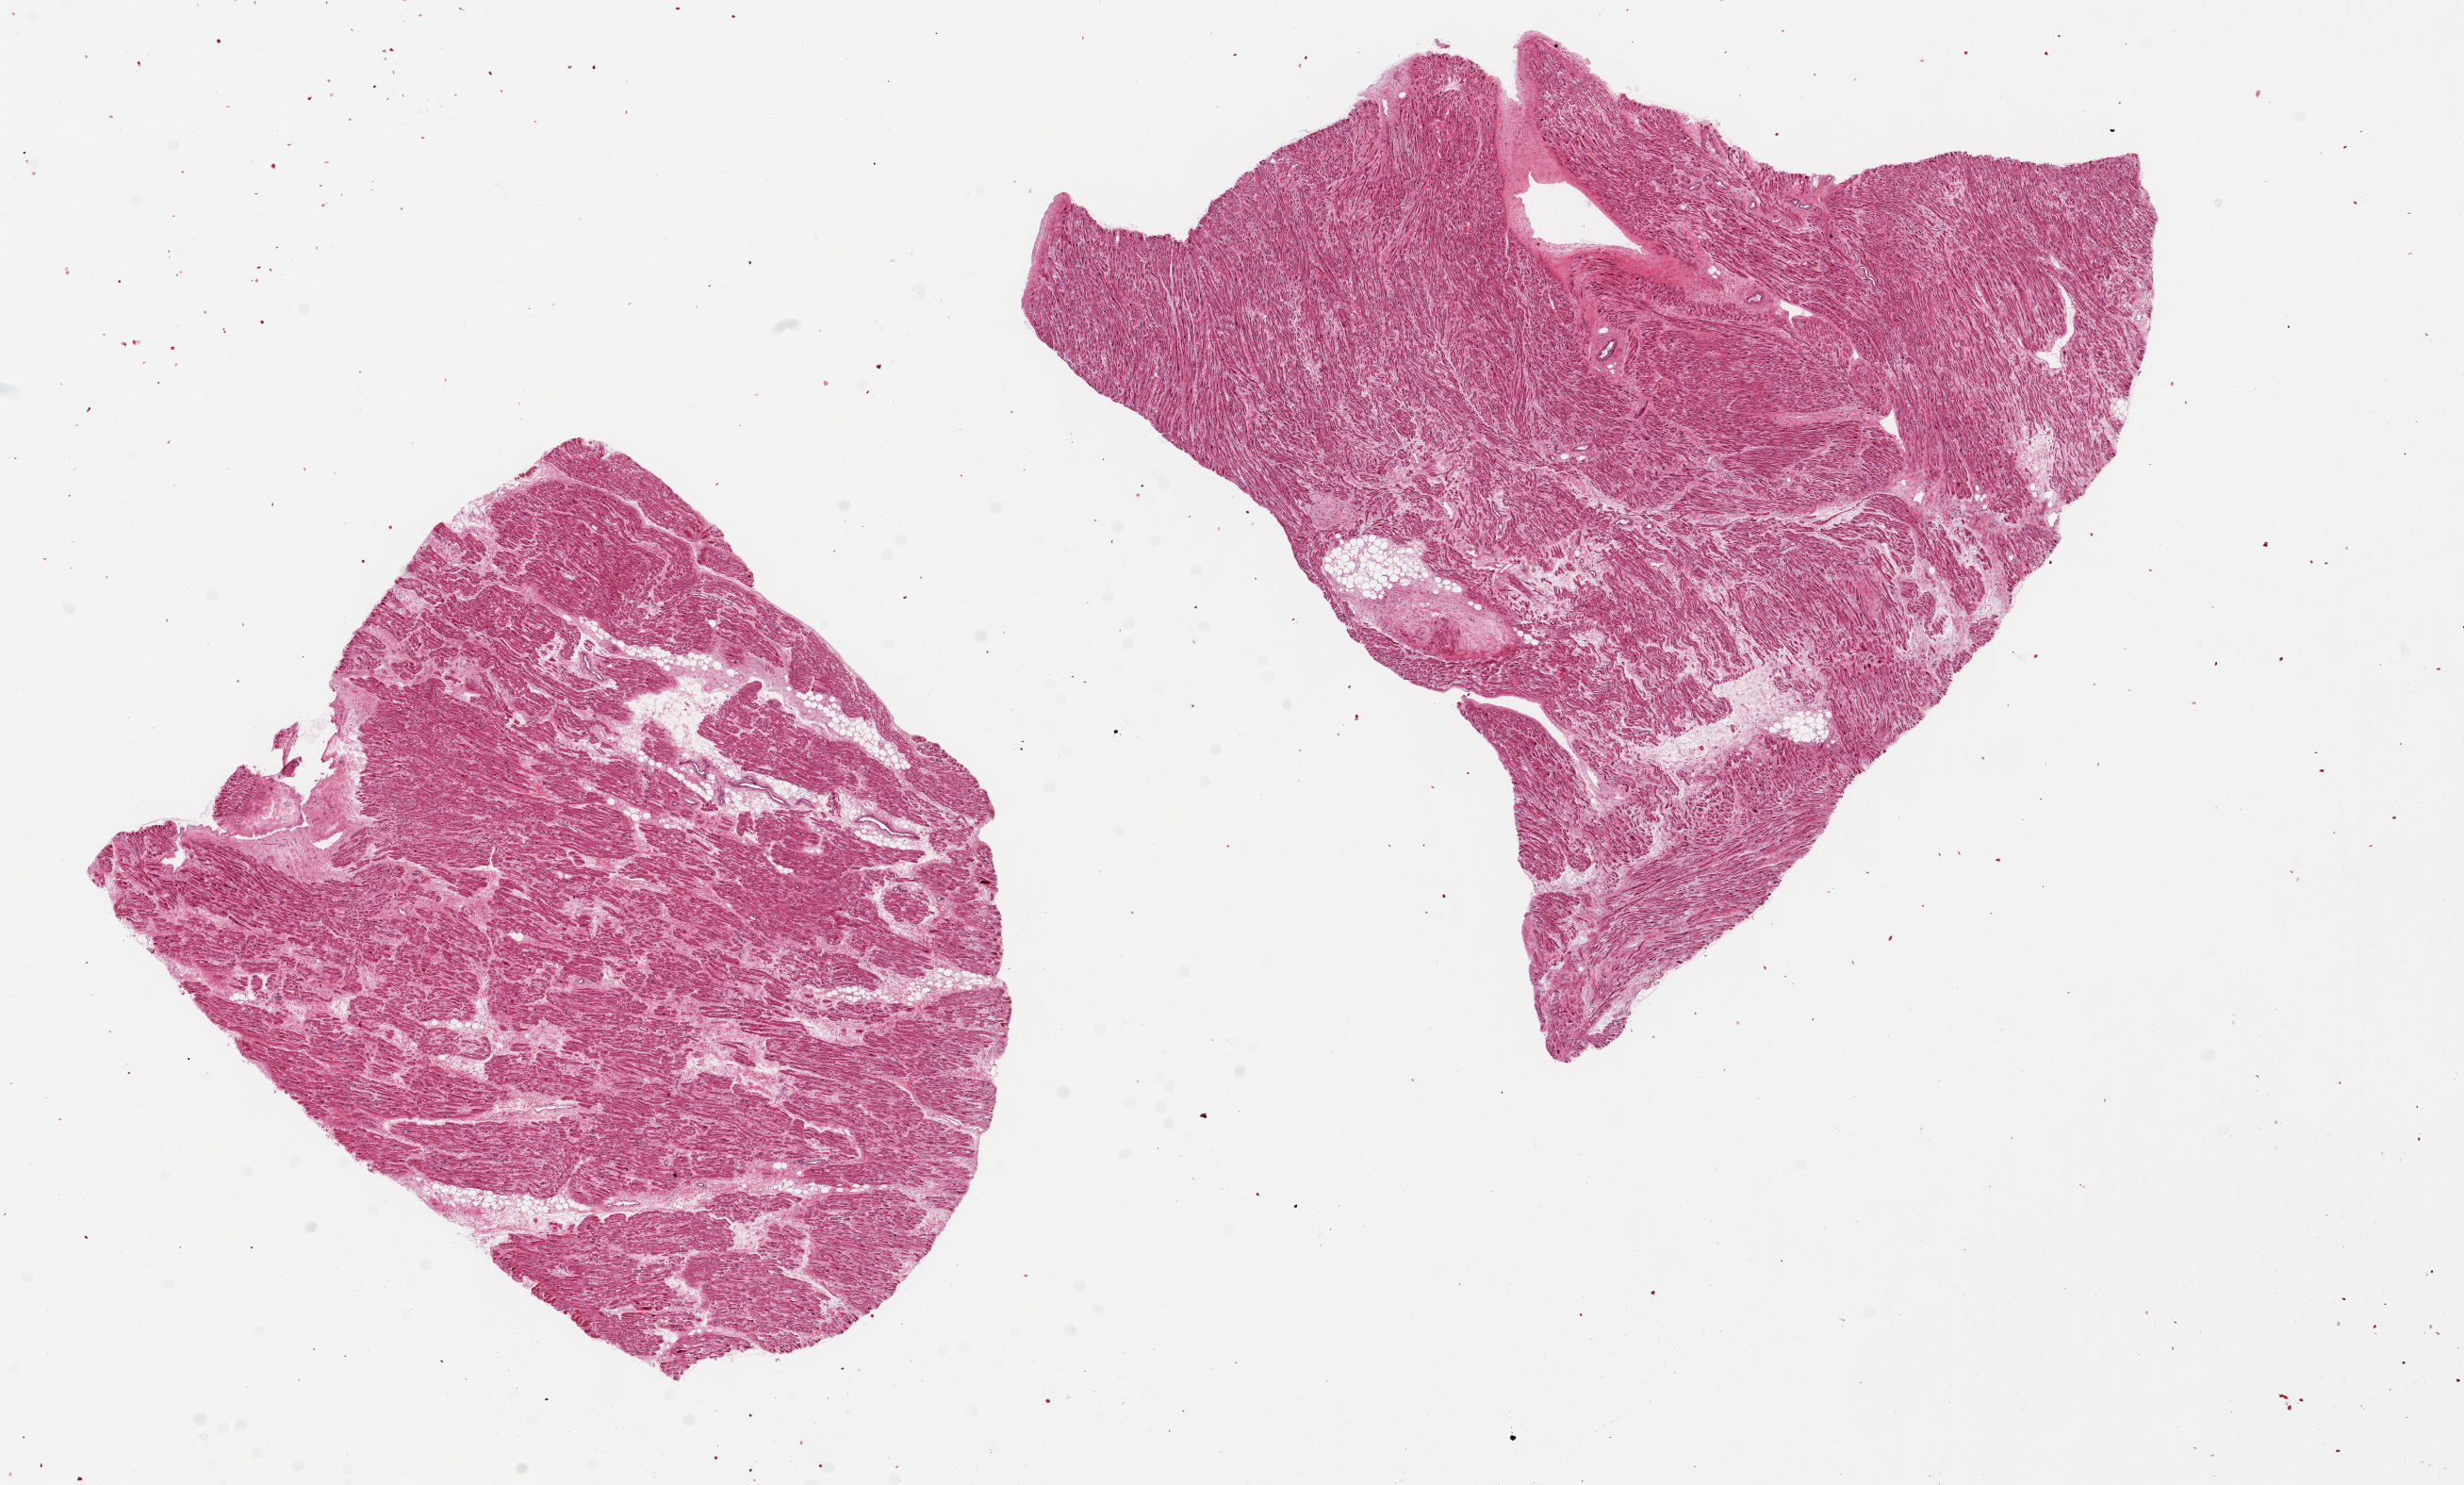
Digitized haematoxylin and eosin-stained section, a low-resolution overview of the entire scanned area, about 20.7 x 12.5 mm; PAXgene-fixed paraffin-embedded (PFPE) section; target tissue: auricular appendage; donor tissue sample. Donor sex: female.
Review note (as recorded): 2 pieces 7.5x8 & 6.5x6; no significant fibrosis.